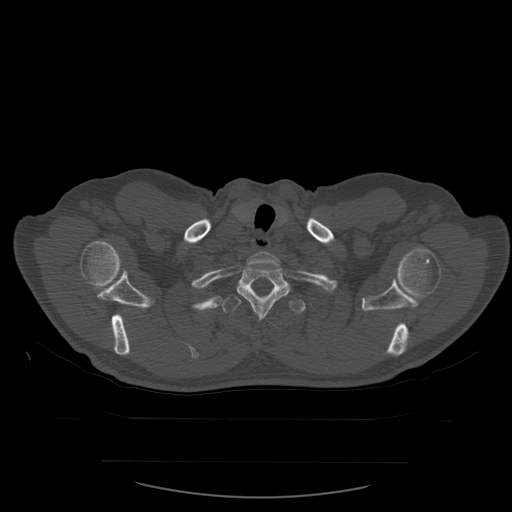
CT including the spine, one axial slice. Position 473 of 590 along the scan axis. Bone window (W 1800 / L 400 HU). 512 × 512 image matrix, field of view 479 × 479 mm. Patient age 71 years. Case-level facts recorded for this patient, not image findings: primary cancer: lung.
Outlined on this slice (semi-automatically segmented with operator editing):
- T1 vertebra: bounding box <247,252,282,269> (left, top, right, bottom; pixels)
- T2 vertebra: <237,264,290,320>
- T3 vertebra: <222,293,306,317>